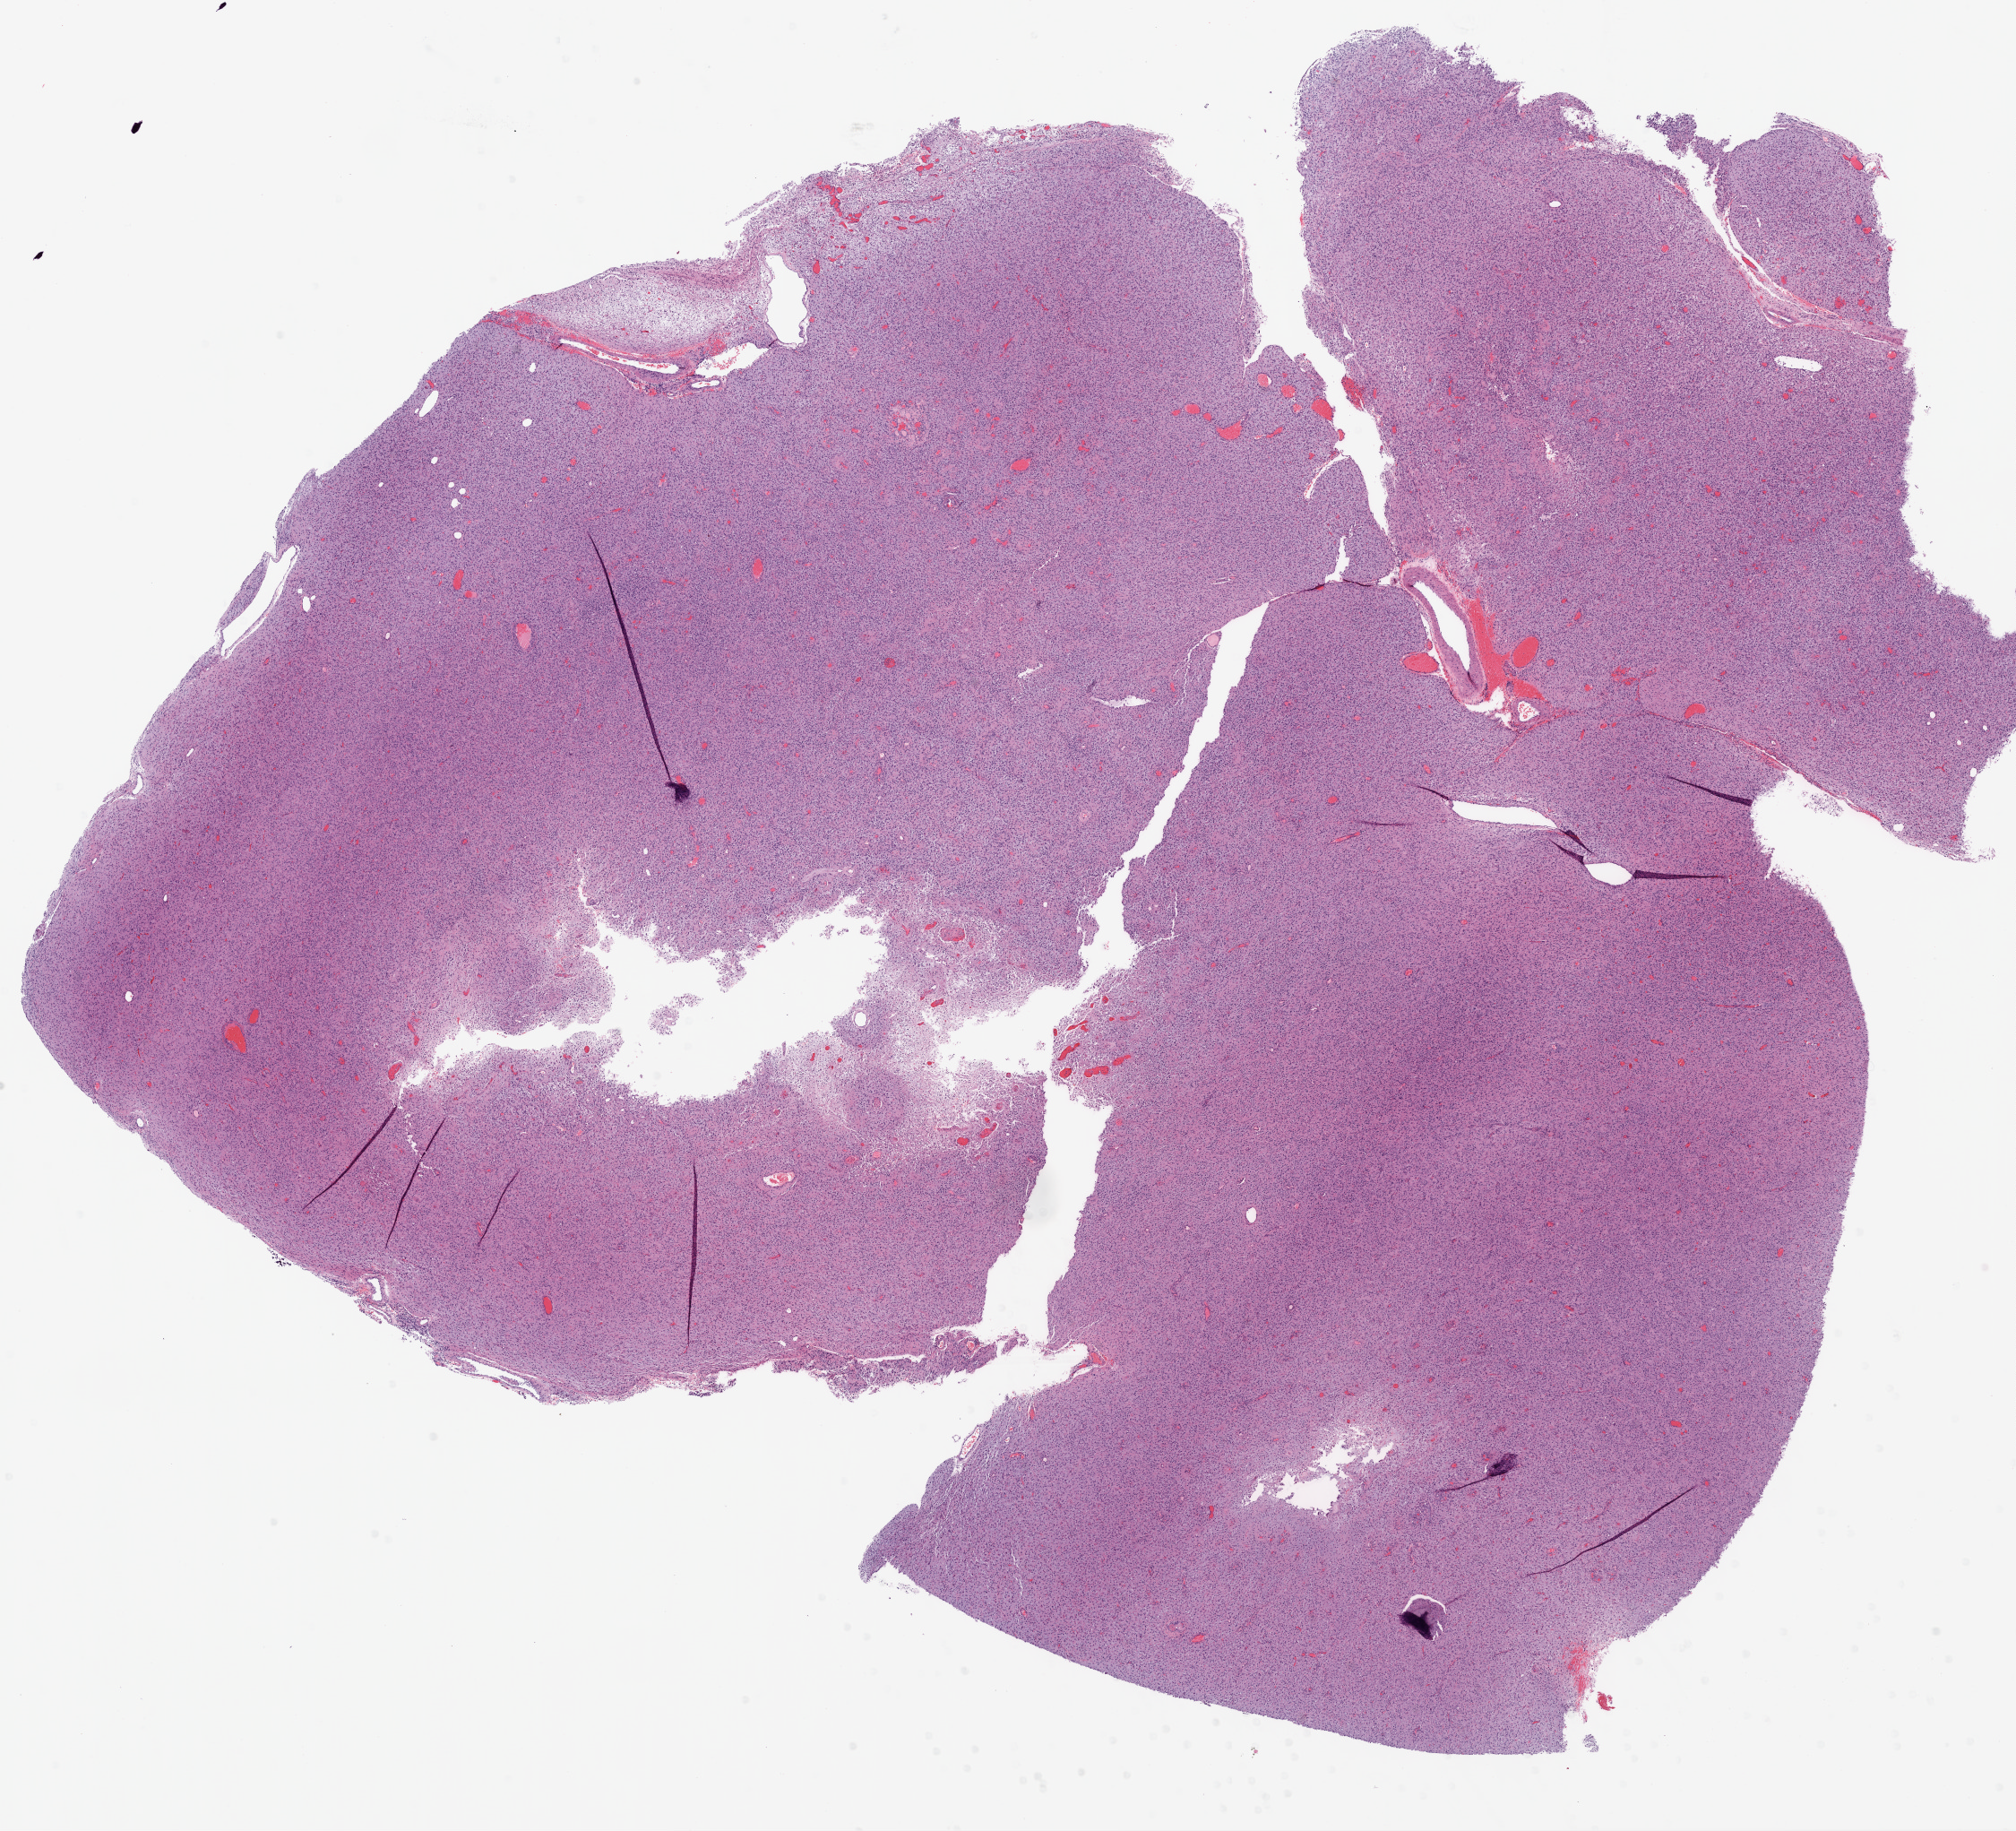
Whole-slide histology image, H&E-stained — a low-resolution overview of the entire scanned area, about 18.1 x 16.4 mm (acquisition: 20x scan). Formalin-fixed paraffin-embedded (FFPE) diagnostic section. Primary tumour sample from the brain. Patient: male, age at initial diagnosis 57 years.
- diagnosis: Glioblastoma